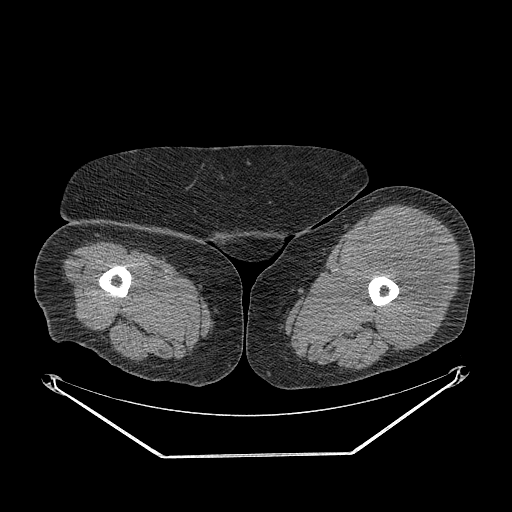
CT of an extremity soft-tissue mass (from a PET/CT study), one axial slice. Slice 234 of 267 in the series (ordered by position). Reconstruction kernel STANDARD. 140 kVp. Soft-tissue window (W 400 / L 40 HU). 512 × 512 image matrix. Female patient. Case-level facts recorded for this patient, not image findings: histological type: undifferentiated – high grade; grade: high; site of the primary tumour: left thigh.
Structures marked on this image (expert contour drawn on MRI and transferred to this co-registered scan by the dataset authors):
- gross tumour volume including surrounding oedema: bounding box (x1, y1, x2, y2) in pixels: (352, 217, 449, 350)
- gross tumour volume (mass): (352, 217, 449, 350)